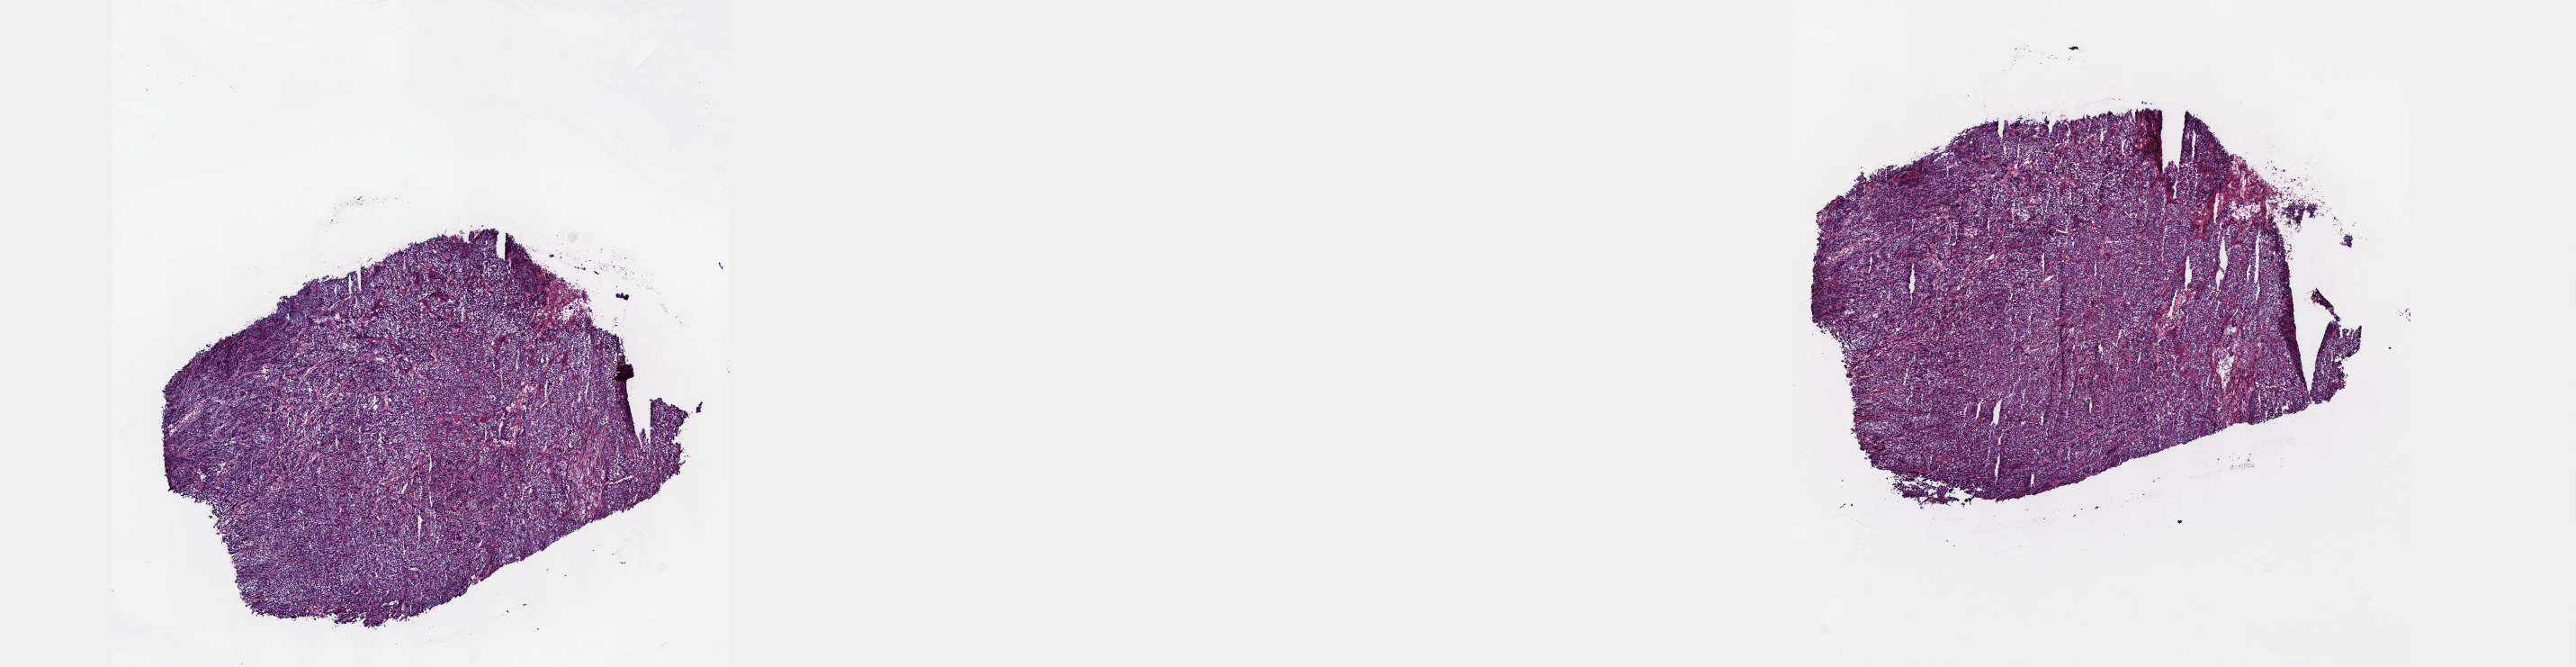
Digitized Hematoxylin and eosin (H&E) stained tissue section (whole slide) — low-resolution overview of the scanned area, about 23.1 x 6.0 mm. Frozen section from the top of the tissue portion. Primary tumour sample from the bladder. Female patient; age at initial diagnosis 88 years. Histologic grade: high grade. Composition of this section per pathologist review: tumour cells 100%, tumour nuclei 80%, normal cells 0%, stromal cells 0%, necrosis 0%. Infiltration values recorded for this section: lymphocyte infiltration 2%, monocyte infiltration 0%, neutrophil infiltration 0%.
• AJCC pathologic stage: III
• histologic diagnosis: Papillary transitional cell carcinoma